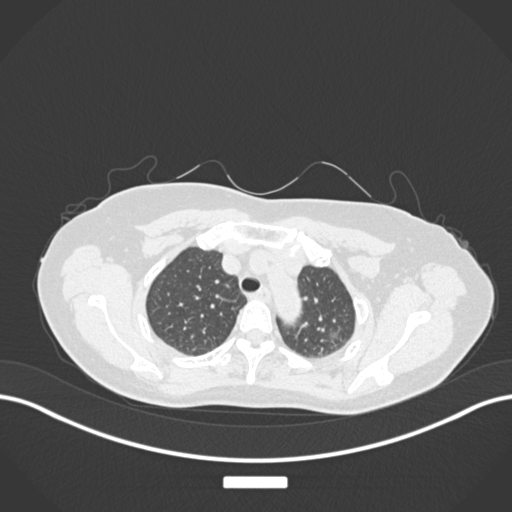
Chest CT, one axial slice. Position 138 of 181 along the scan axis. Reconstruction kernel B30f. 120 kVp. Lung window (W 1500 / L -600 HU). 1 mm slice thickness. 512 × 512 image matrix. Patient: female, 58 years. From the clinical record (not read from this slice): clinical TNM (as recorded): T1c N0 M0.
Annotated regions visible in this slice (bounding box drawn by a radiologist):
- lung tumour (recorded histology: adenocarcinoma): bounding box <319,323,344,350> (left, top, right, bottom; pixels)